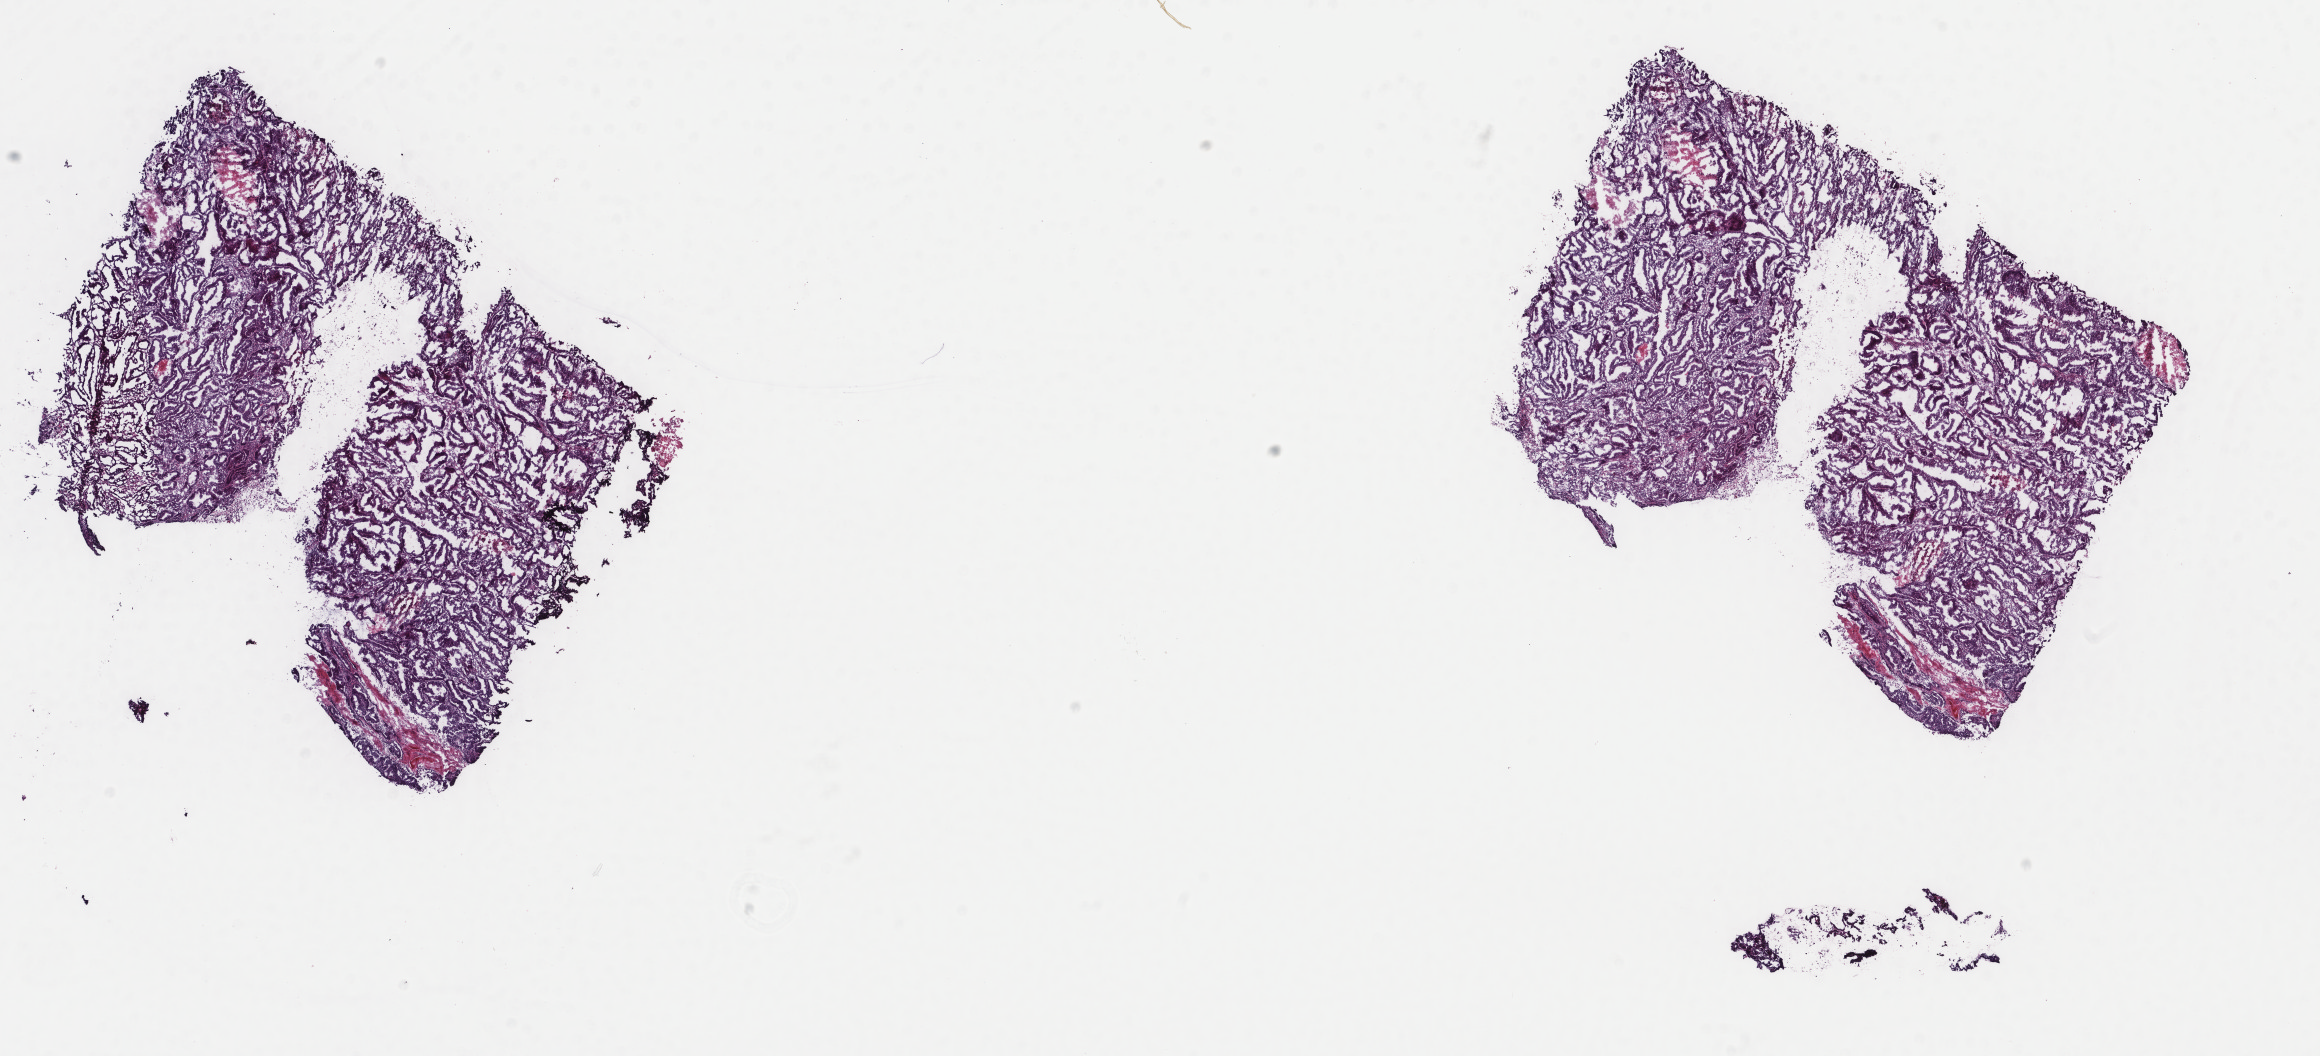
Hematoxylin and eosin (H&E) stained whole-slide image — a low-resolution overview of the entire scanned area, about 18.4 x 8.4 mm (slide scanned at 40x); frozen section from the top of the tissue portion; sample: primary tumour, uterus. Female patient; age at initial diagnosis 53 years. Histologic grade: G2 (moderately differentiated). Slide review estimates, as recorded: tumour cells 100%, tumour nuclei 75%, normal cells 0%, stromal cells 0%, necrosis 0%. Inflammatory infiltration, as recorded: lymphocyte infiltration 0%, monocyte infiltration 0%, neutrophil infiltration 0%.
• FIGO stage: I
• diagnosis: Endometrioid adenocarcinoma, NOS (endometrium)